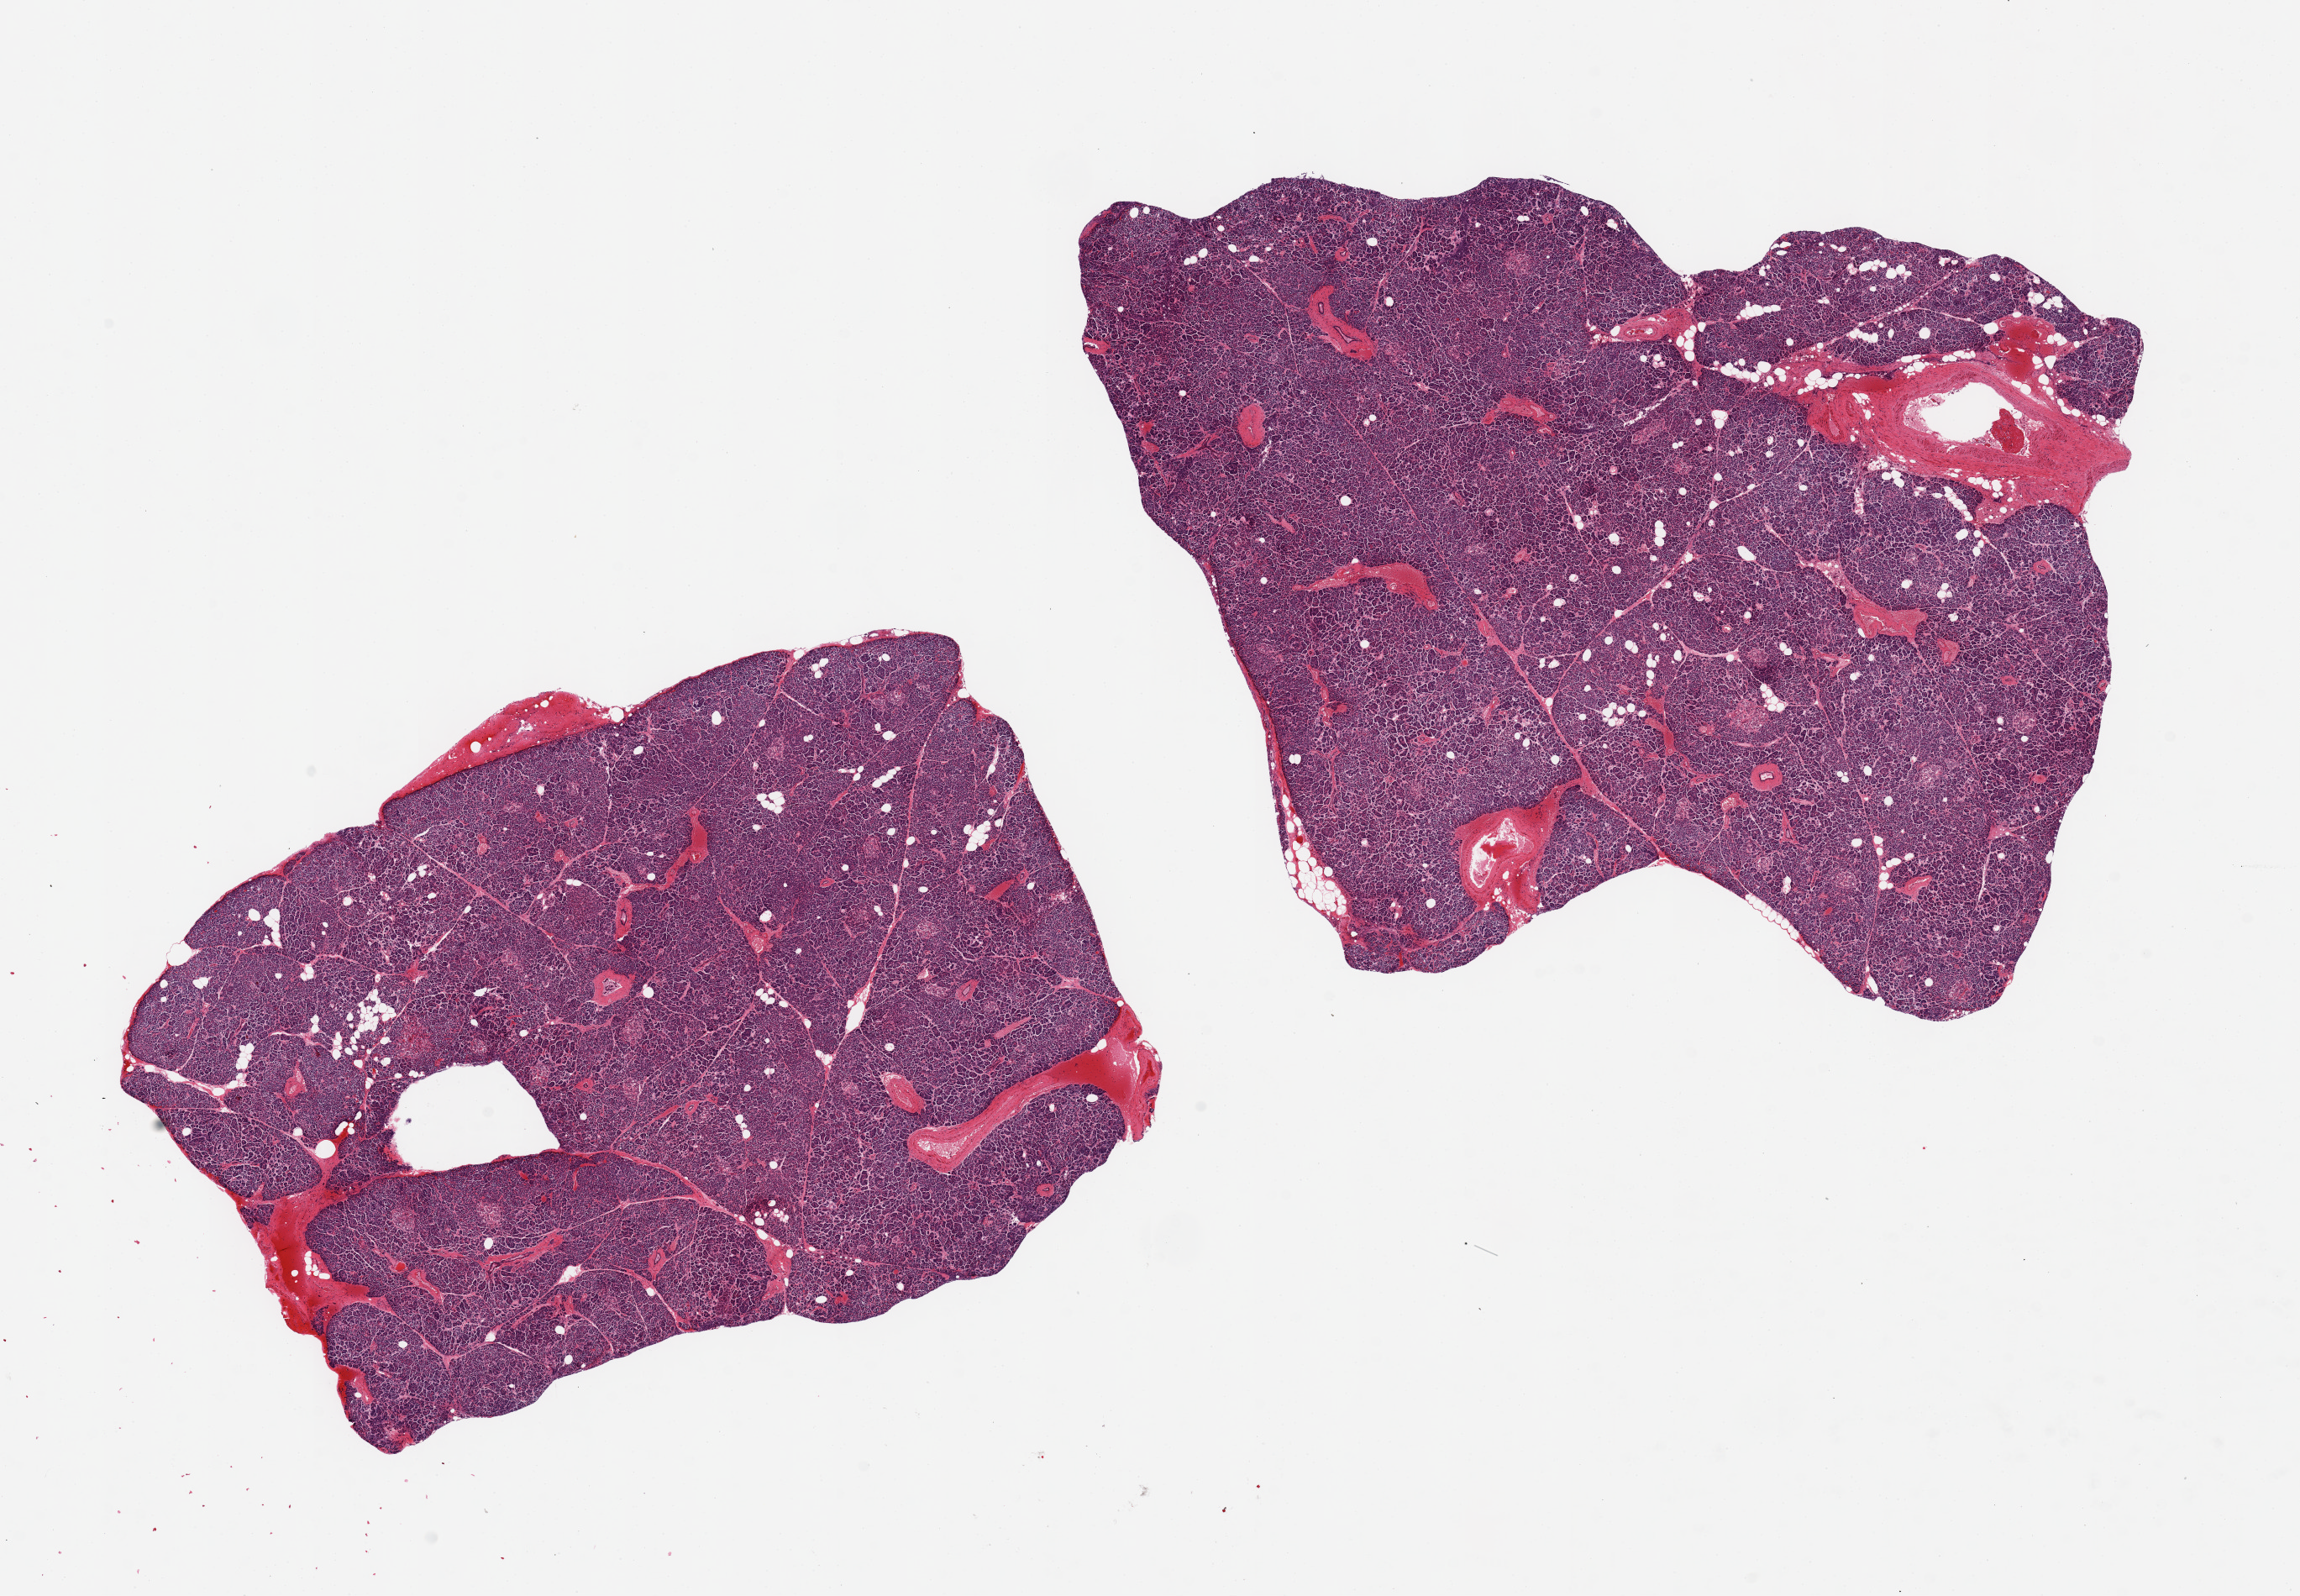
Whole-slide image, hematoxylin and eosin (H&E) stain — whole scanned area (about 21.7 x 15.0 mm) shown as a low-resolution overview. PAXgene-fixed paraffin-embedded (PFPE) section. Target tissue: pancreas. Donor tissue sample. Donor sex: male.
Reviewer comment on this tissue sample: 2 pieces ~9x6mm; Minimal fat, well preserved; Islets rare but visible.